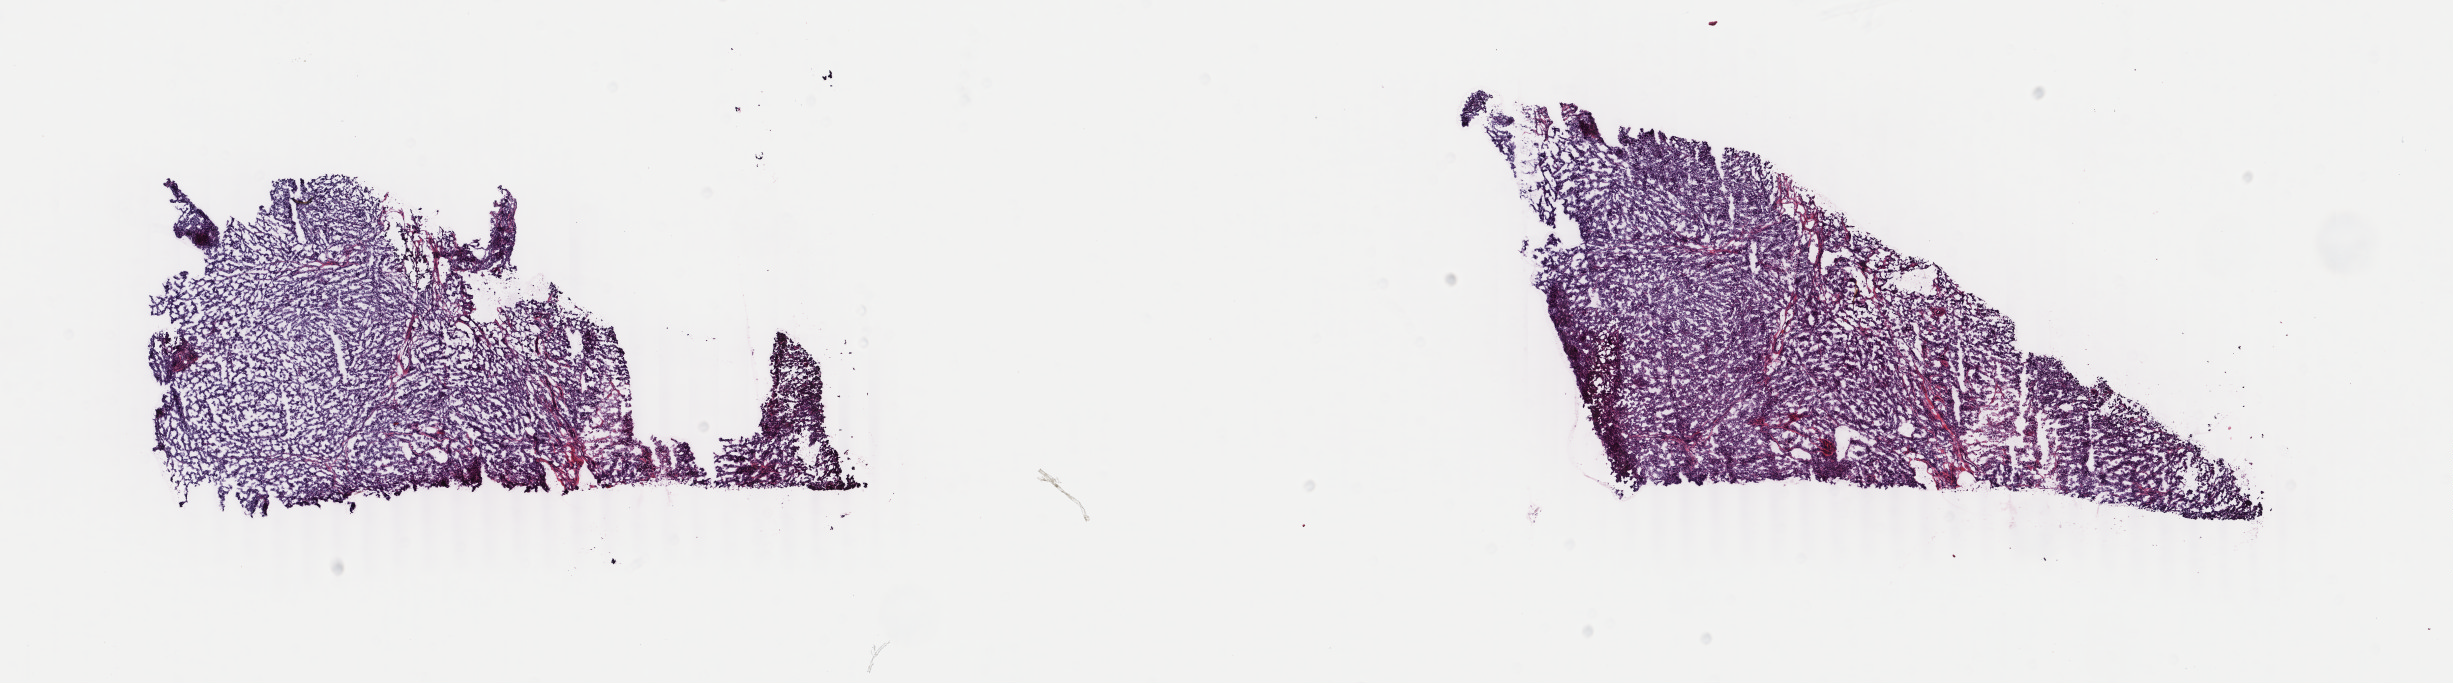
Whole-slide histology image, H&E — shown as a low-resolution overview of the whole scanned area (about 19.5 x 5.4 mm), frozen section, sample: primary tumour, breast. Female, age 42 years at initial diagnosis. Composition of this section per pathologist review: tumour cells 95%, tumour nuclei 95%, normal cells 0%, stromal cells 3%, necrosis 2%. Inflammatory infiltration, as recorded: lymphocyte infiltration 0%, monocyte infiltration 0%, neutrophil infiltration 0%.
AJCC pathologic stage: IIB. Lymph nodes positive (case pathology): 0 of 27 examined. Diagnosis: Infiltrating duct carcinoma, NOS. TNM: T3 N0 (i-) M0. Laterality: right.